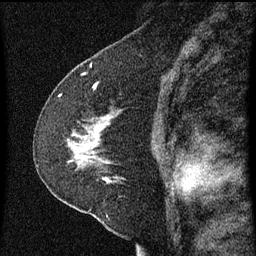
Breast MRI (dynamic contrast-enhanced), one sagittal slice; dynamic contrast-enhanced series, image 2 of 3 at this slice position (ordered by acquisition); 1.5 T; TE 4.2 ms, TR 8 ms; 2 mm slice thickness; 256 × 256 image matrix, field of view 180 × 180 mm. Patient: female, 47 years.
Structures marked on this image (semi-automatic segmentation, software-assisted and operator-edited):
- analysis volume of interest (the breast-tissue region the enhancement analysis was run in; not a lesion): bounding box <36,96,158,213> (left, top, right, bottom; pixels)
- tumour enhancement mask (voxels above the 70 % enhancement threshold inside the analysis volume of interest): <74,134,110,181>